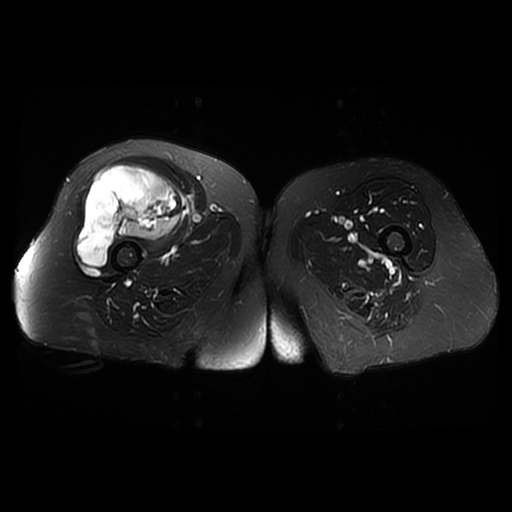
MRI of an extremity soft-tissue mass, one axial slice; slice 26 of 42 in the series (ordered by position); T2-weighted fat-saturated; 6 mm slice thickness; 512 × 512 image matrix, field of view 440 × 440 mm. Female patient. Case-level facts recorded for this patient, not image findings: histological type: pleiomorphic undifferentiated sarcoma; grade: high; site of the primary tumour: right quadricep.
Structures marked on this image (manually delineated by an expert):
- gross tumour volume including surrounding oedema: bounding box (x1, y1, x2, y2) in pixels: (76, 166, 181, 266)
- gross tumour volume (mass): (76, 166, 181, 266)